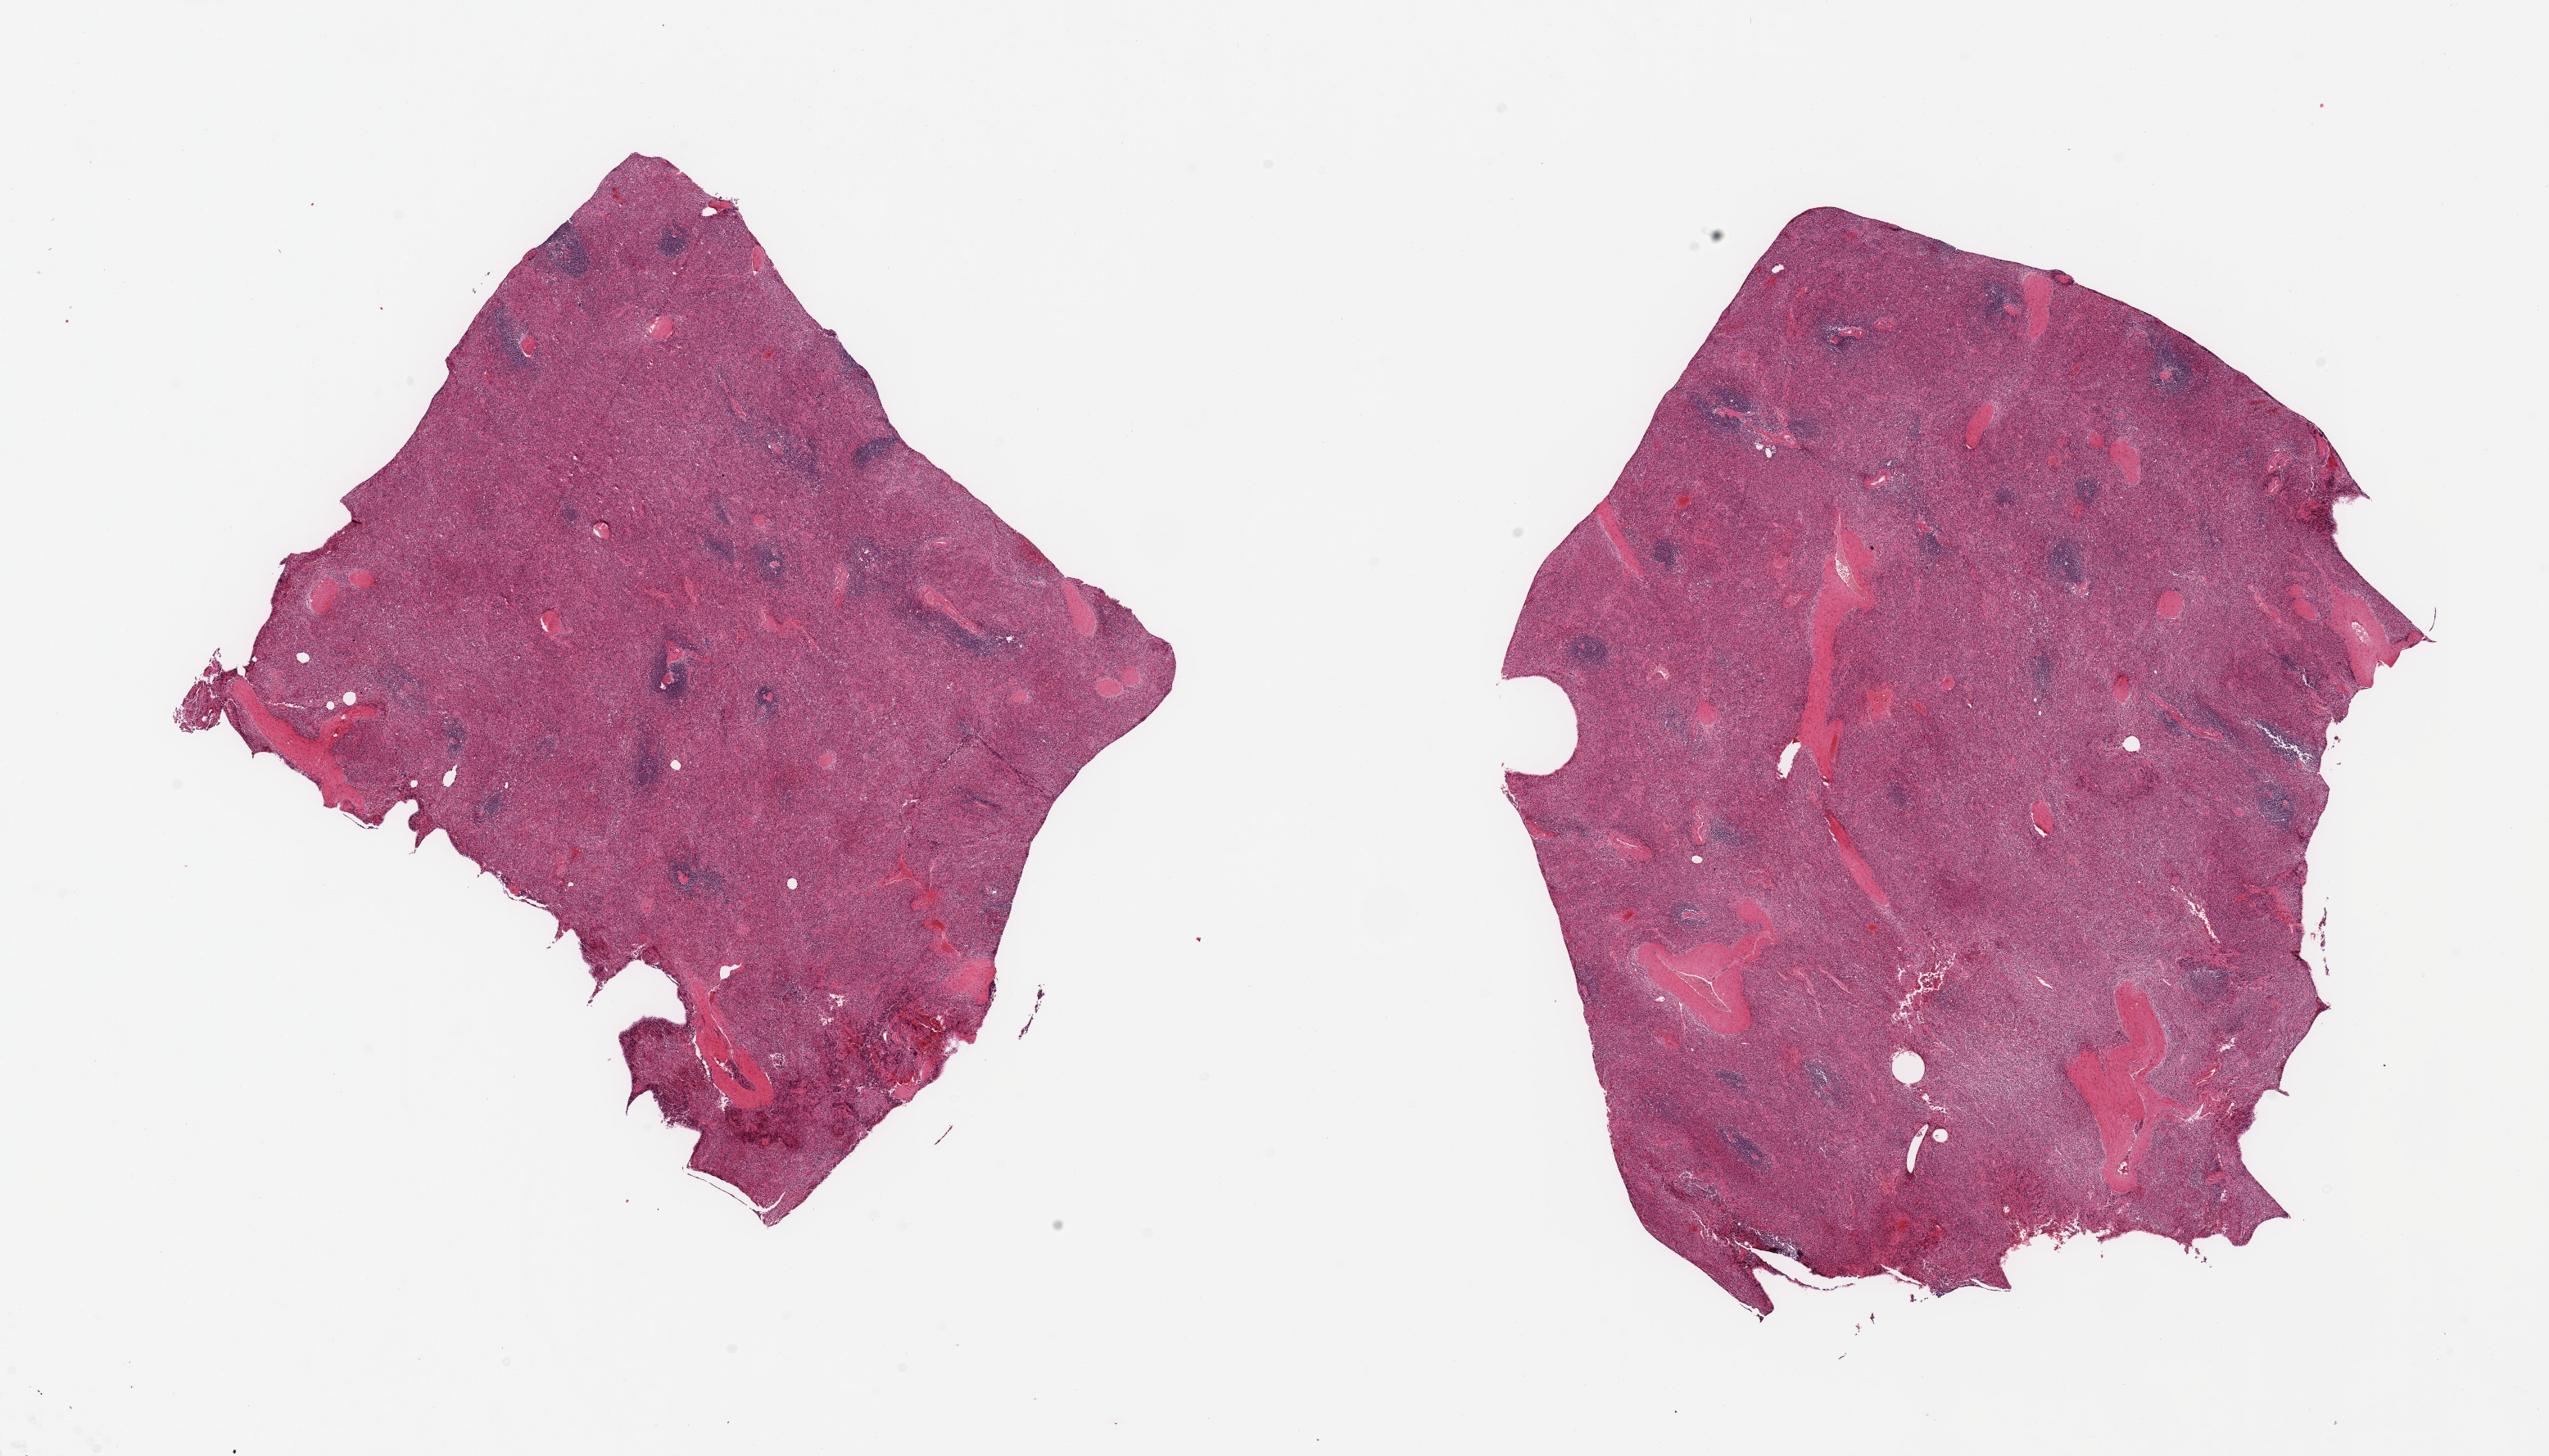
Digitized H&E-stained section, brightfield — shown as a low-resolution overview of the whole scanned area (about 24.6 x 14.1 mm, acquisition: 20x scan); PAXgene-fixed paraffin-embedded (PFPE) section; target tissue: spleen; donor tissue sample. Donor: female.
Reviewer comment on this tissue sample: 2 pieces; slight congestion.